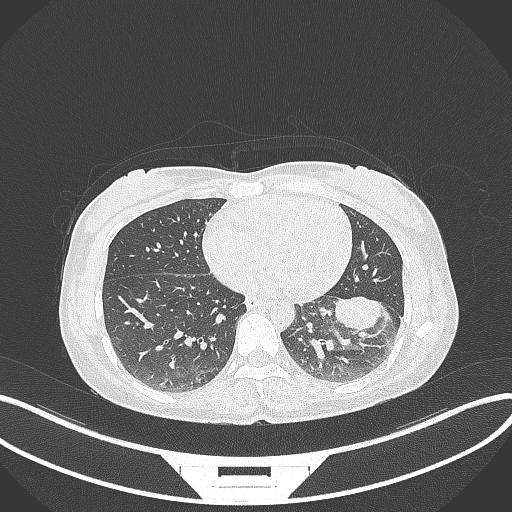
Chest CT, one axial slice. Position 19 of 244 along the scan axis. Reconstruction kernel B70f. 120 kVp. Lung window (W 1500 / L -600 HU). 512 × 512 image matrix. Patient: female, 41 years. Case-level facts recorded for this patient, not image findings: clinical TNM (as recorded): T2a N3 M1b.
Annotated regions visible in this slice (rectangle marked by the reading radiologist):
- lung tumour (recorded histology: adenocarcinoma): bounding box [x1, y1, x2, y2] px = [333, 293, 385, 333]